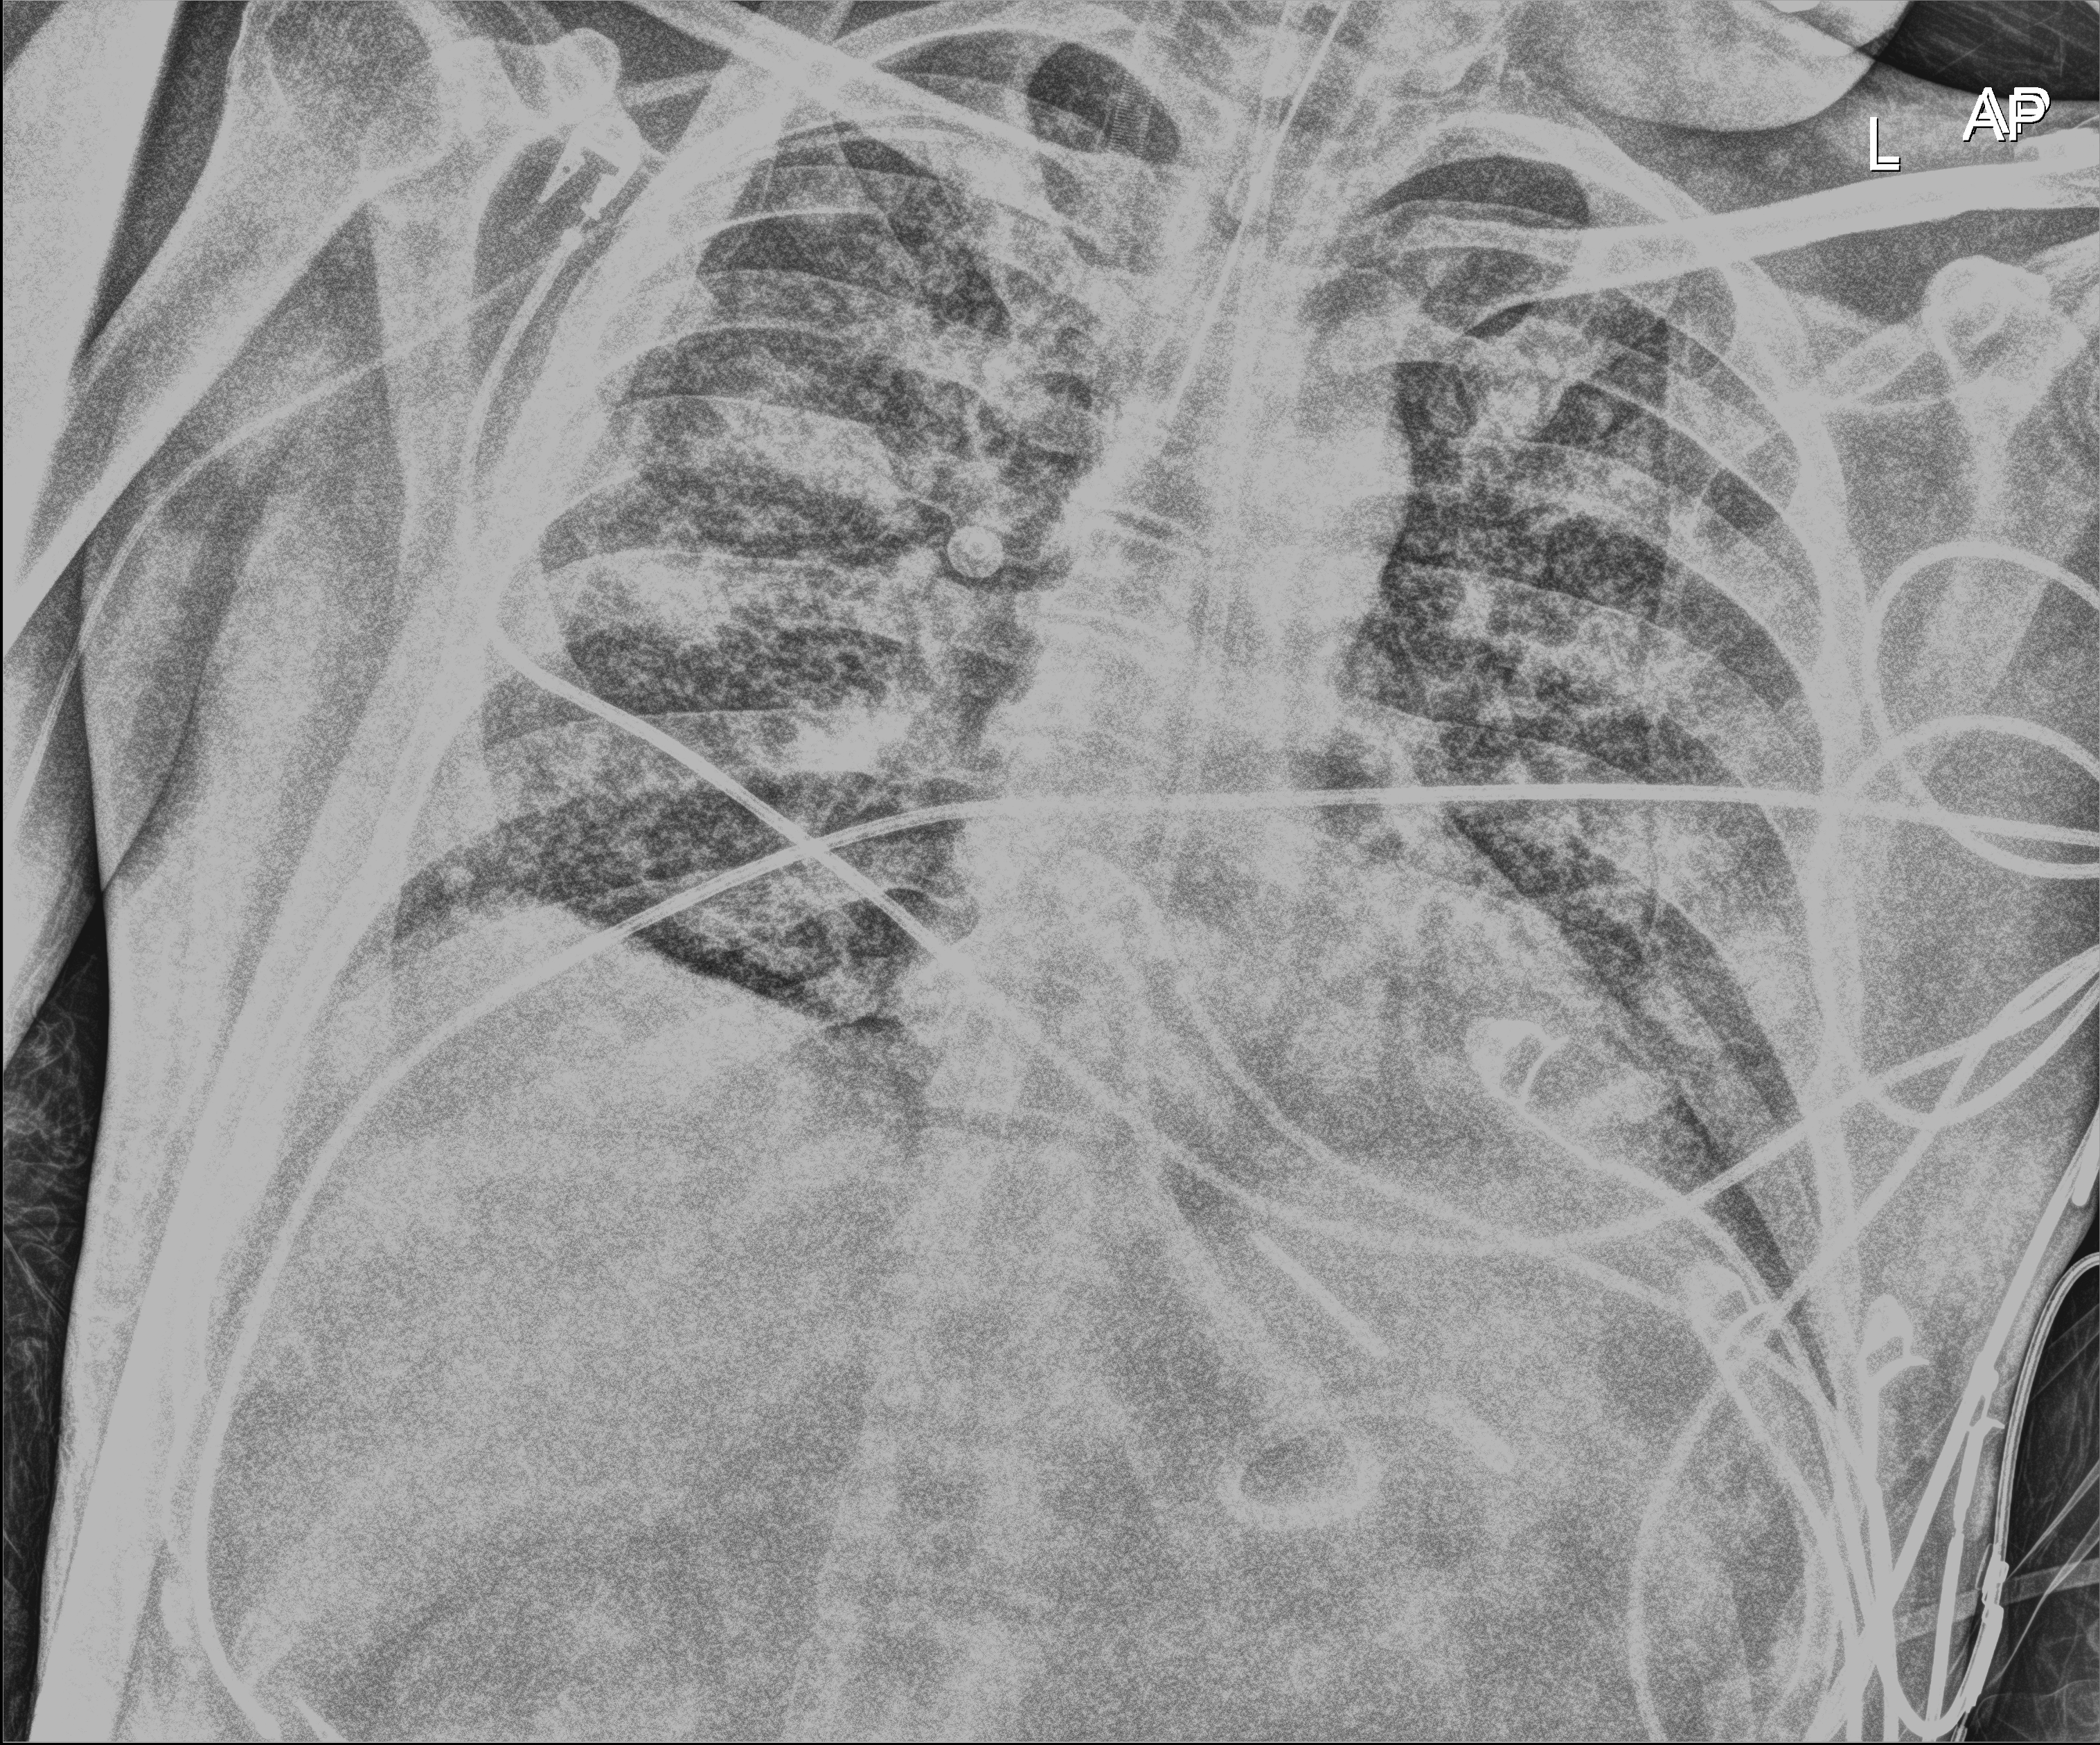
Bedside chest radiograph (digital radiography), anteroposterior (AP) projection. Patient hospitalised with COVID-19; male, aged 18–59 years.
Admission-level facts for this patient (not findings on this image; timing relative to this image not recorded): admitted to intensive care during this hospital stay: yes; chronic kidney disease (admission record): no; length of hospital stay: 42 days.